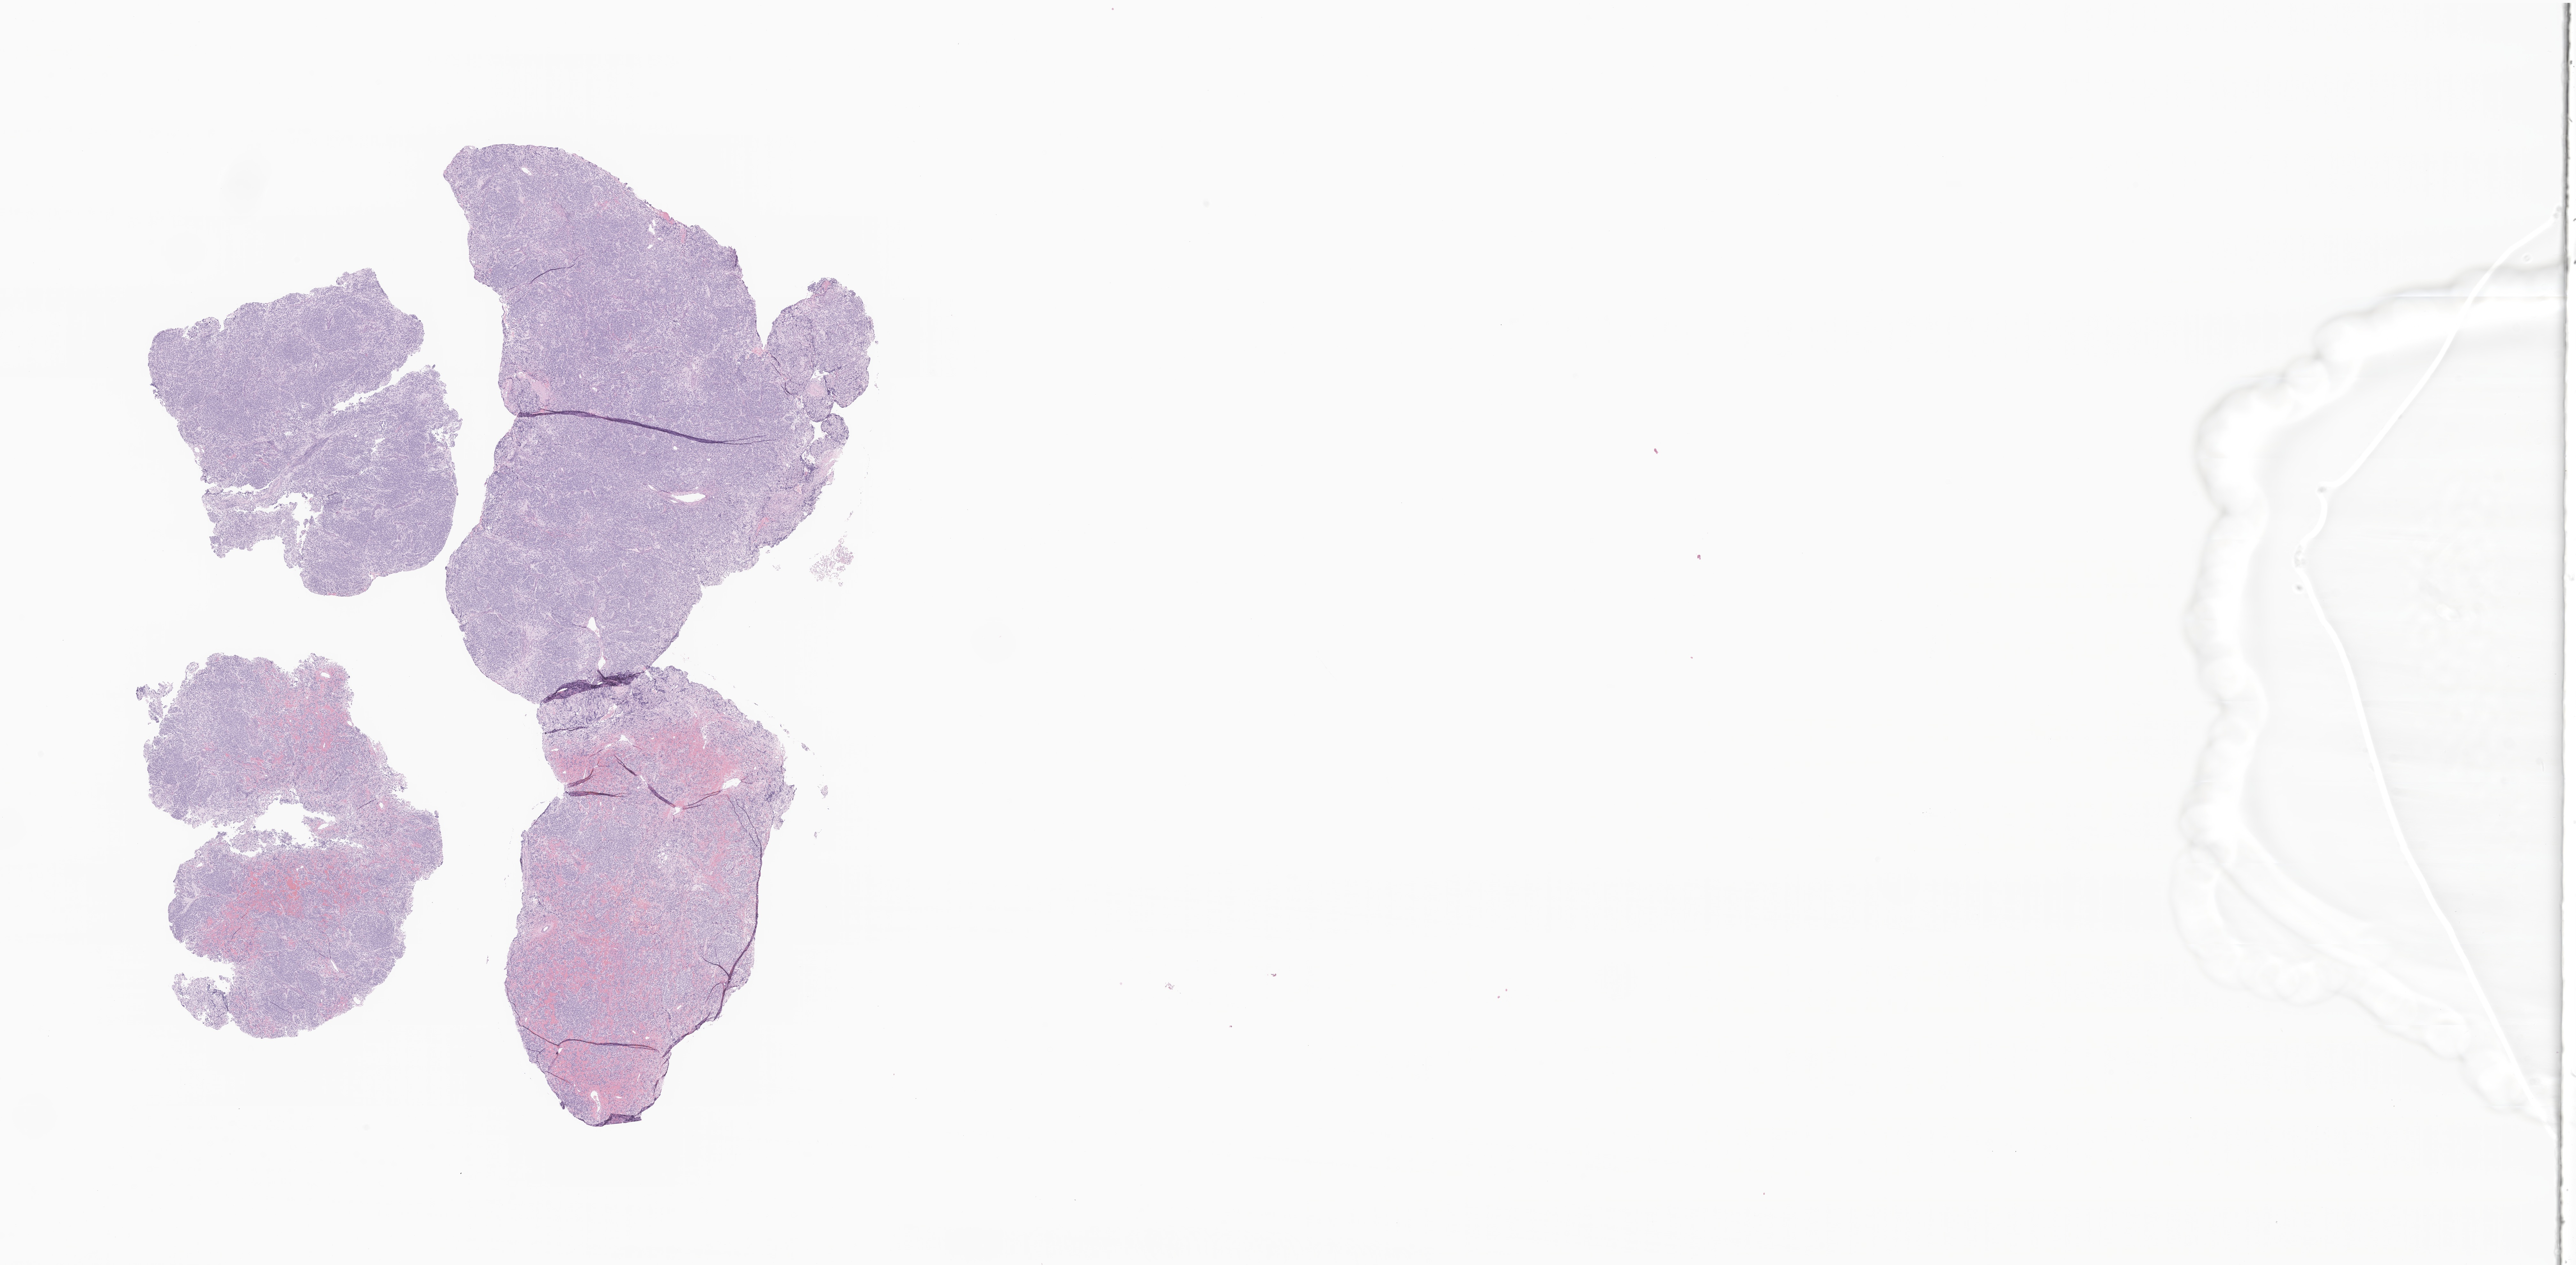
Whole-slide image, haematoxylin and eosin stain of tumor tissue from the abdomen — whole scanned area (about 34.0 x 16.7 mm) shown as a low-resolution overview, formalin-fixed, paraffin-embedded (FFPE) tissue. Patient male; age 59 days.
Diagnosis: Neuroblastoma, NOS.